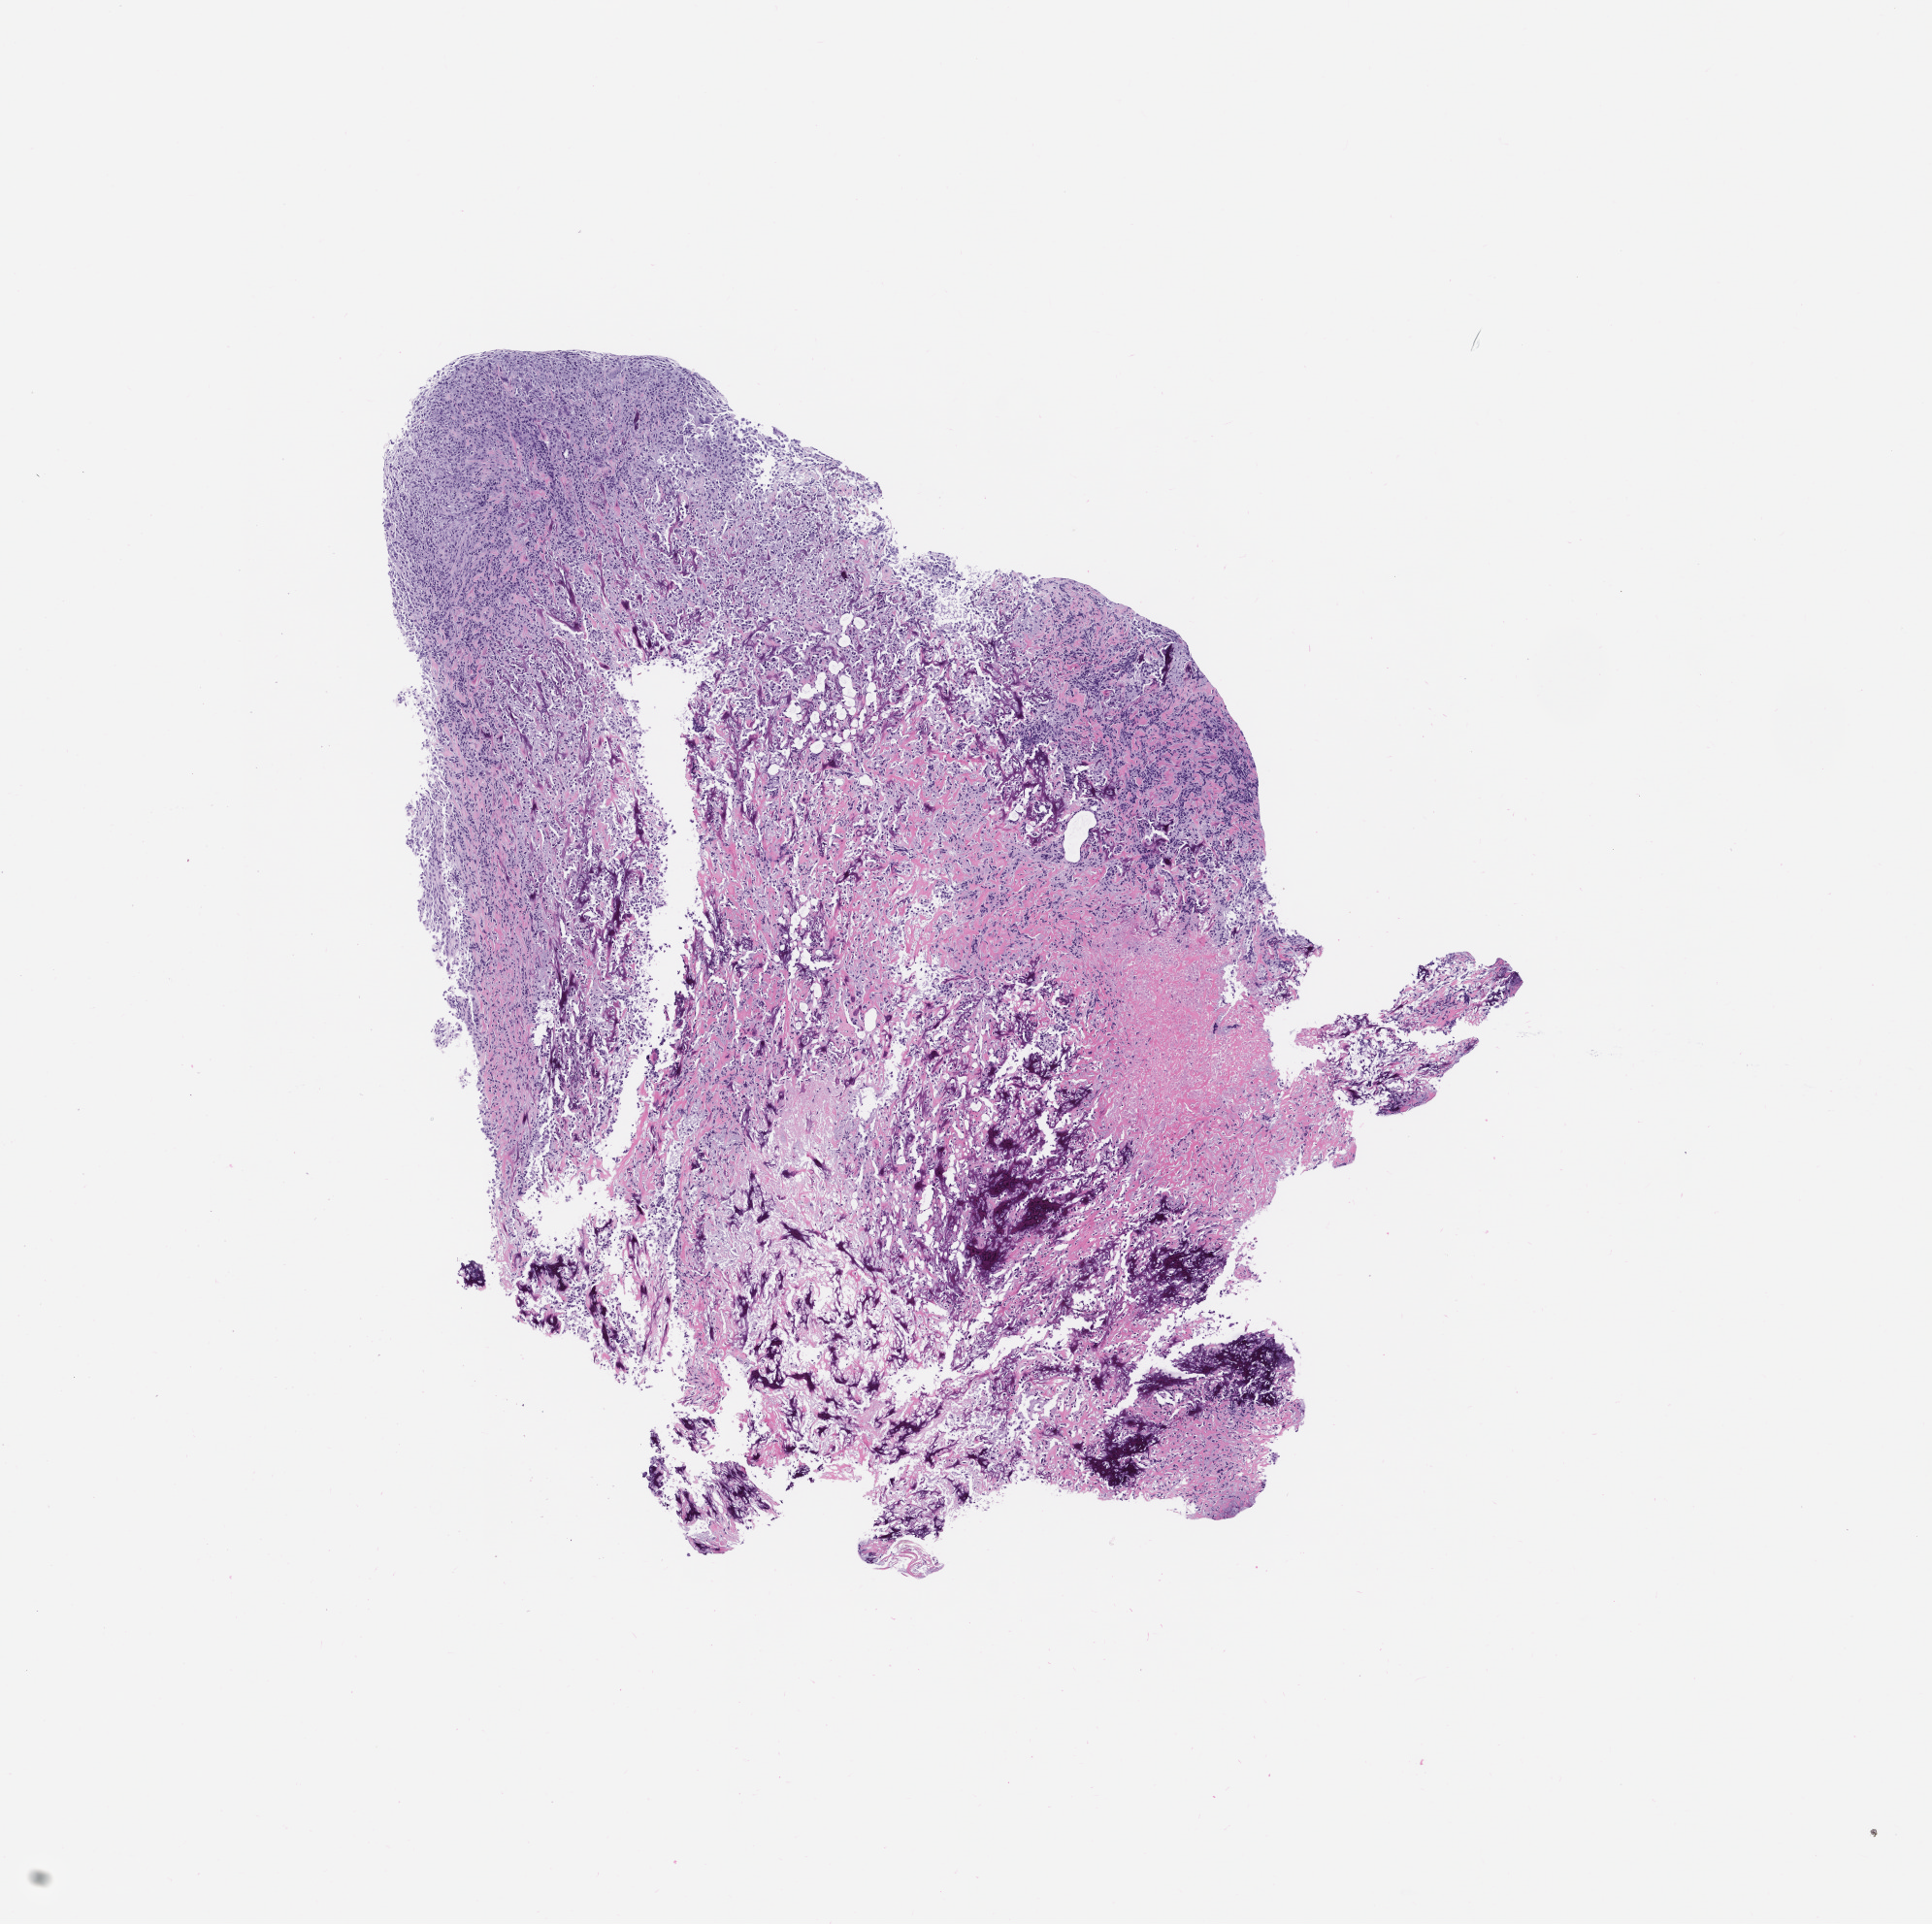
Haematoxylin and eosin whole-slide image of a patient-derived xenograft (PDX) tumor grown in a mouse, passage 0 — whole scanned area (about 8.0 x 7.9 mm) shown as a low-resolution overview; formalin-fixed paraffin-embedded section; originating tumor site category: bone.
Originating patient diagnosis: Osteosarcoma.